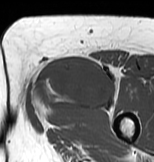
MRI of an extremity soft-tissue mass, one axial slice. Slice 36 of 83 in the series (ordered by position). MR volume resampled by the dataset authors to the PET/CT grid (not the native acquisition matrix). 154 × 162 image matrix, field of view 150 × 158 mm. Female patient. Case-level facts recorded for this patient, not image findings: histological type: myxofibrosarcoma; grade: intermediate; site of the primary tumour: left thigh.
Annotated regions visible in this slice (expert contour drawn on MRI and transferred to this co-registered scan by the dataset authors):
- gross tumour volume including surrounding oedema: box from (x=28, y=54) to (x=120, y=124) px
- gross tumour volume (mass): (x=33, y=54)–(x=113, y=108)